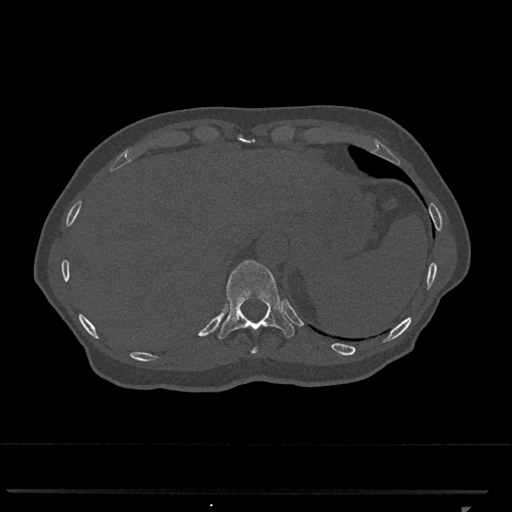
CT including the spine, one axial slice; slice 525 of 793 in the series (ordered by position); reconstruction kernel Br40s/3; 120 kVp; bone window (W 1800 / L 400 HU); 0.5 mm slice thickness; 512 × 512 image matrix, field of view 380 × 380 mm. Female patient, age 62 years. Case-level facts recorded for this patient, not image findings: primary cancer: renal.
Structures marked on this image (semi-automatically segmented with operator editing):
- T10 vertebra: bounding box [x1, y1, x2, y2] px = [251, 347, 257, 354]
- T11 vertebra: [218, 260, 295, 339]